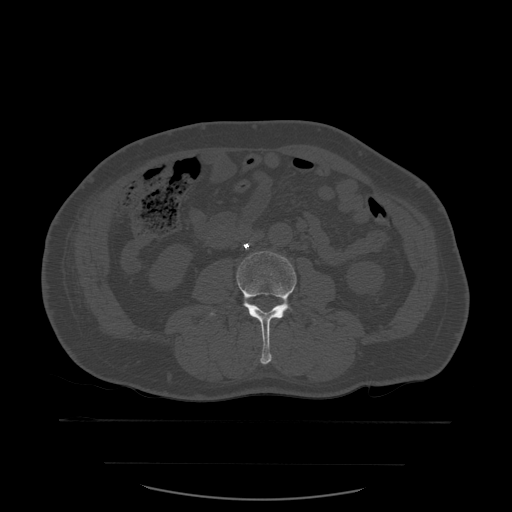
CT including the spine, one axial slice. Position 190 of 590 along the scan axis. Bone window (W 1800 / L 400 HU). 1.25 mm slice thickness. 512 × 512 image matrix, field of view 479 × 479 mm. Patient age 71 years. Case-level facts recorded for this patient, not image findings: primary cancer: lung; vertebrae with lytic lesions (as recorded): T1, T2, L5, S1.
Outlined on this slice (semi-automatically segmented with operator editing):
- L3 vertebra: bounding box <210,251,297,365> (left, top, right, bottom; pixels)